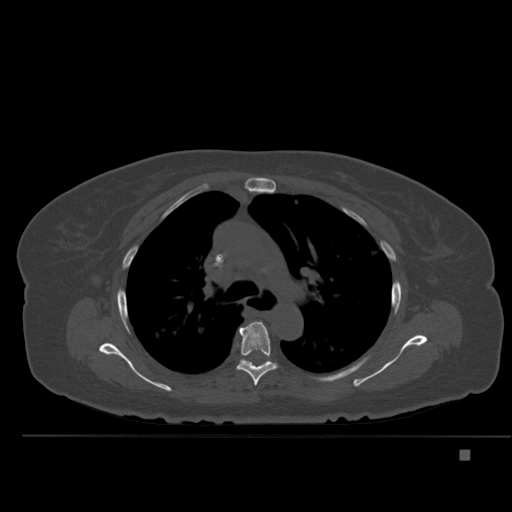
CT including the spine, one axial slice; slice 353 of 477 in the series (ordered by position); bone window (W 1800 / L 400 HU); 512 × 512 image matrix, field of view 422 × 422 mm. Female patient, age 74 years. From the clinical record (not read from this slice): primary cancer: colon.
Structures marked on this image (semi-automatic segmentation, software-assisted and operator-edited):
- T5 vertebra: box from (x=236, y=321) to (x=277, y=386) px
- T6 vertebra: (x=245, y=359)–(x=249, y=362)